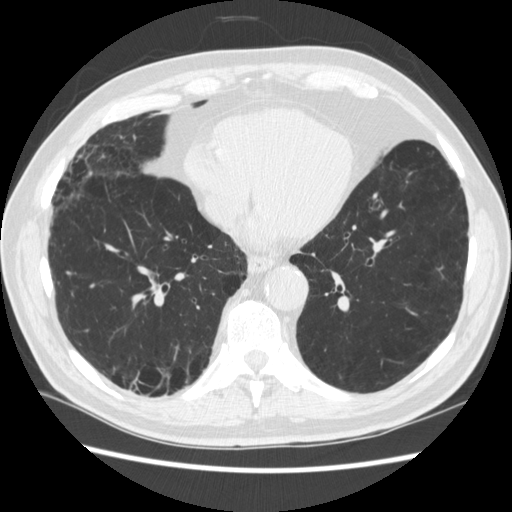
Chest CT (low-dose screening protocol), one axial image, third screening round (two years after baseline), lung window (W 1500 / L -600 HU), 1.25 mm slice thickness, 120 kVp, slice 168 of 266 in the series, 512 × 512 image matrix, field of view 360 × 360 mm. Male, age 70 years at enrolment. Former smoker at enrolment.
Lesion marked by an expert reader, bounding box <132,358,175,411> (left, top, right, bottom; pixels). The screening reader recorded 4 non-calcified nodules or masses ≥4 mm on this exam; which of them this box marks is not recorded. Later outcome: lung cancer diagnosed 253 days after this screen — squamous cell carcinoma, NOS, right upper lobe, poorly differentiated (G3), stage IV (AJCC 6th edition).